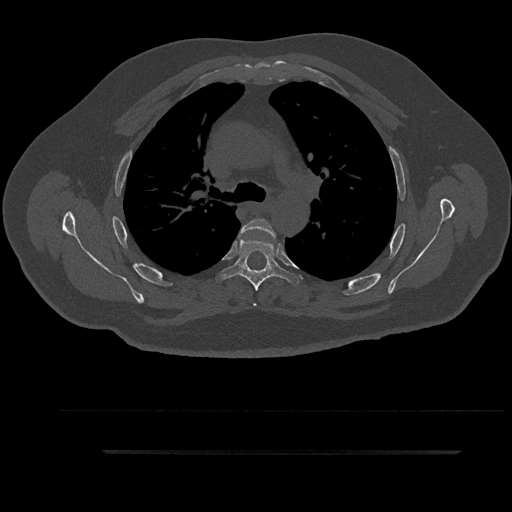
CT including the spine, one axial slice. Slice 637 of 797 in the series (ordered by position). Reconstruction kernel Br40s/3. Bone window (W 1800 / L 400 HU). 0.5 mm slice thickness. 512 × 512 image matrix. Patient: male, 63 years. From the clinical record (not read from this slice): primary cancer: renal; vertebrae with lytic lesions (as recorded): T8.
Structures marked on this image (semi-automatically segmented with operator editing):
- T4 vertebra: bounding box (x1, y1, x2, y2) in pixels: (238, 218, 278, 306)
- T5 vertebra: (216, 236, 299, 291)